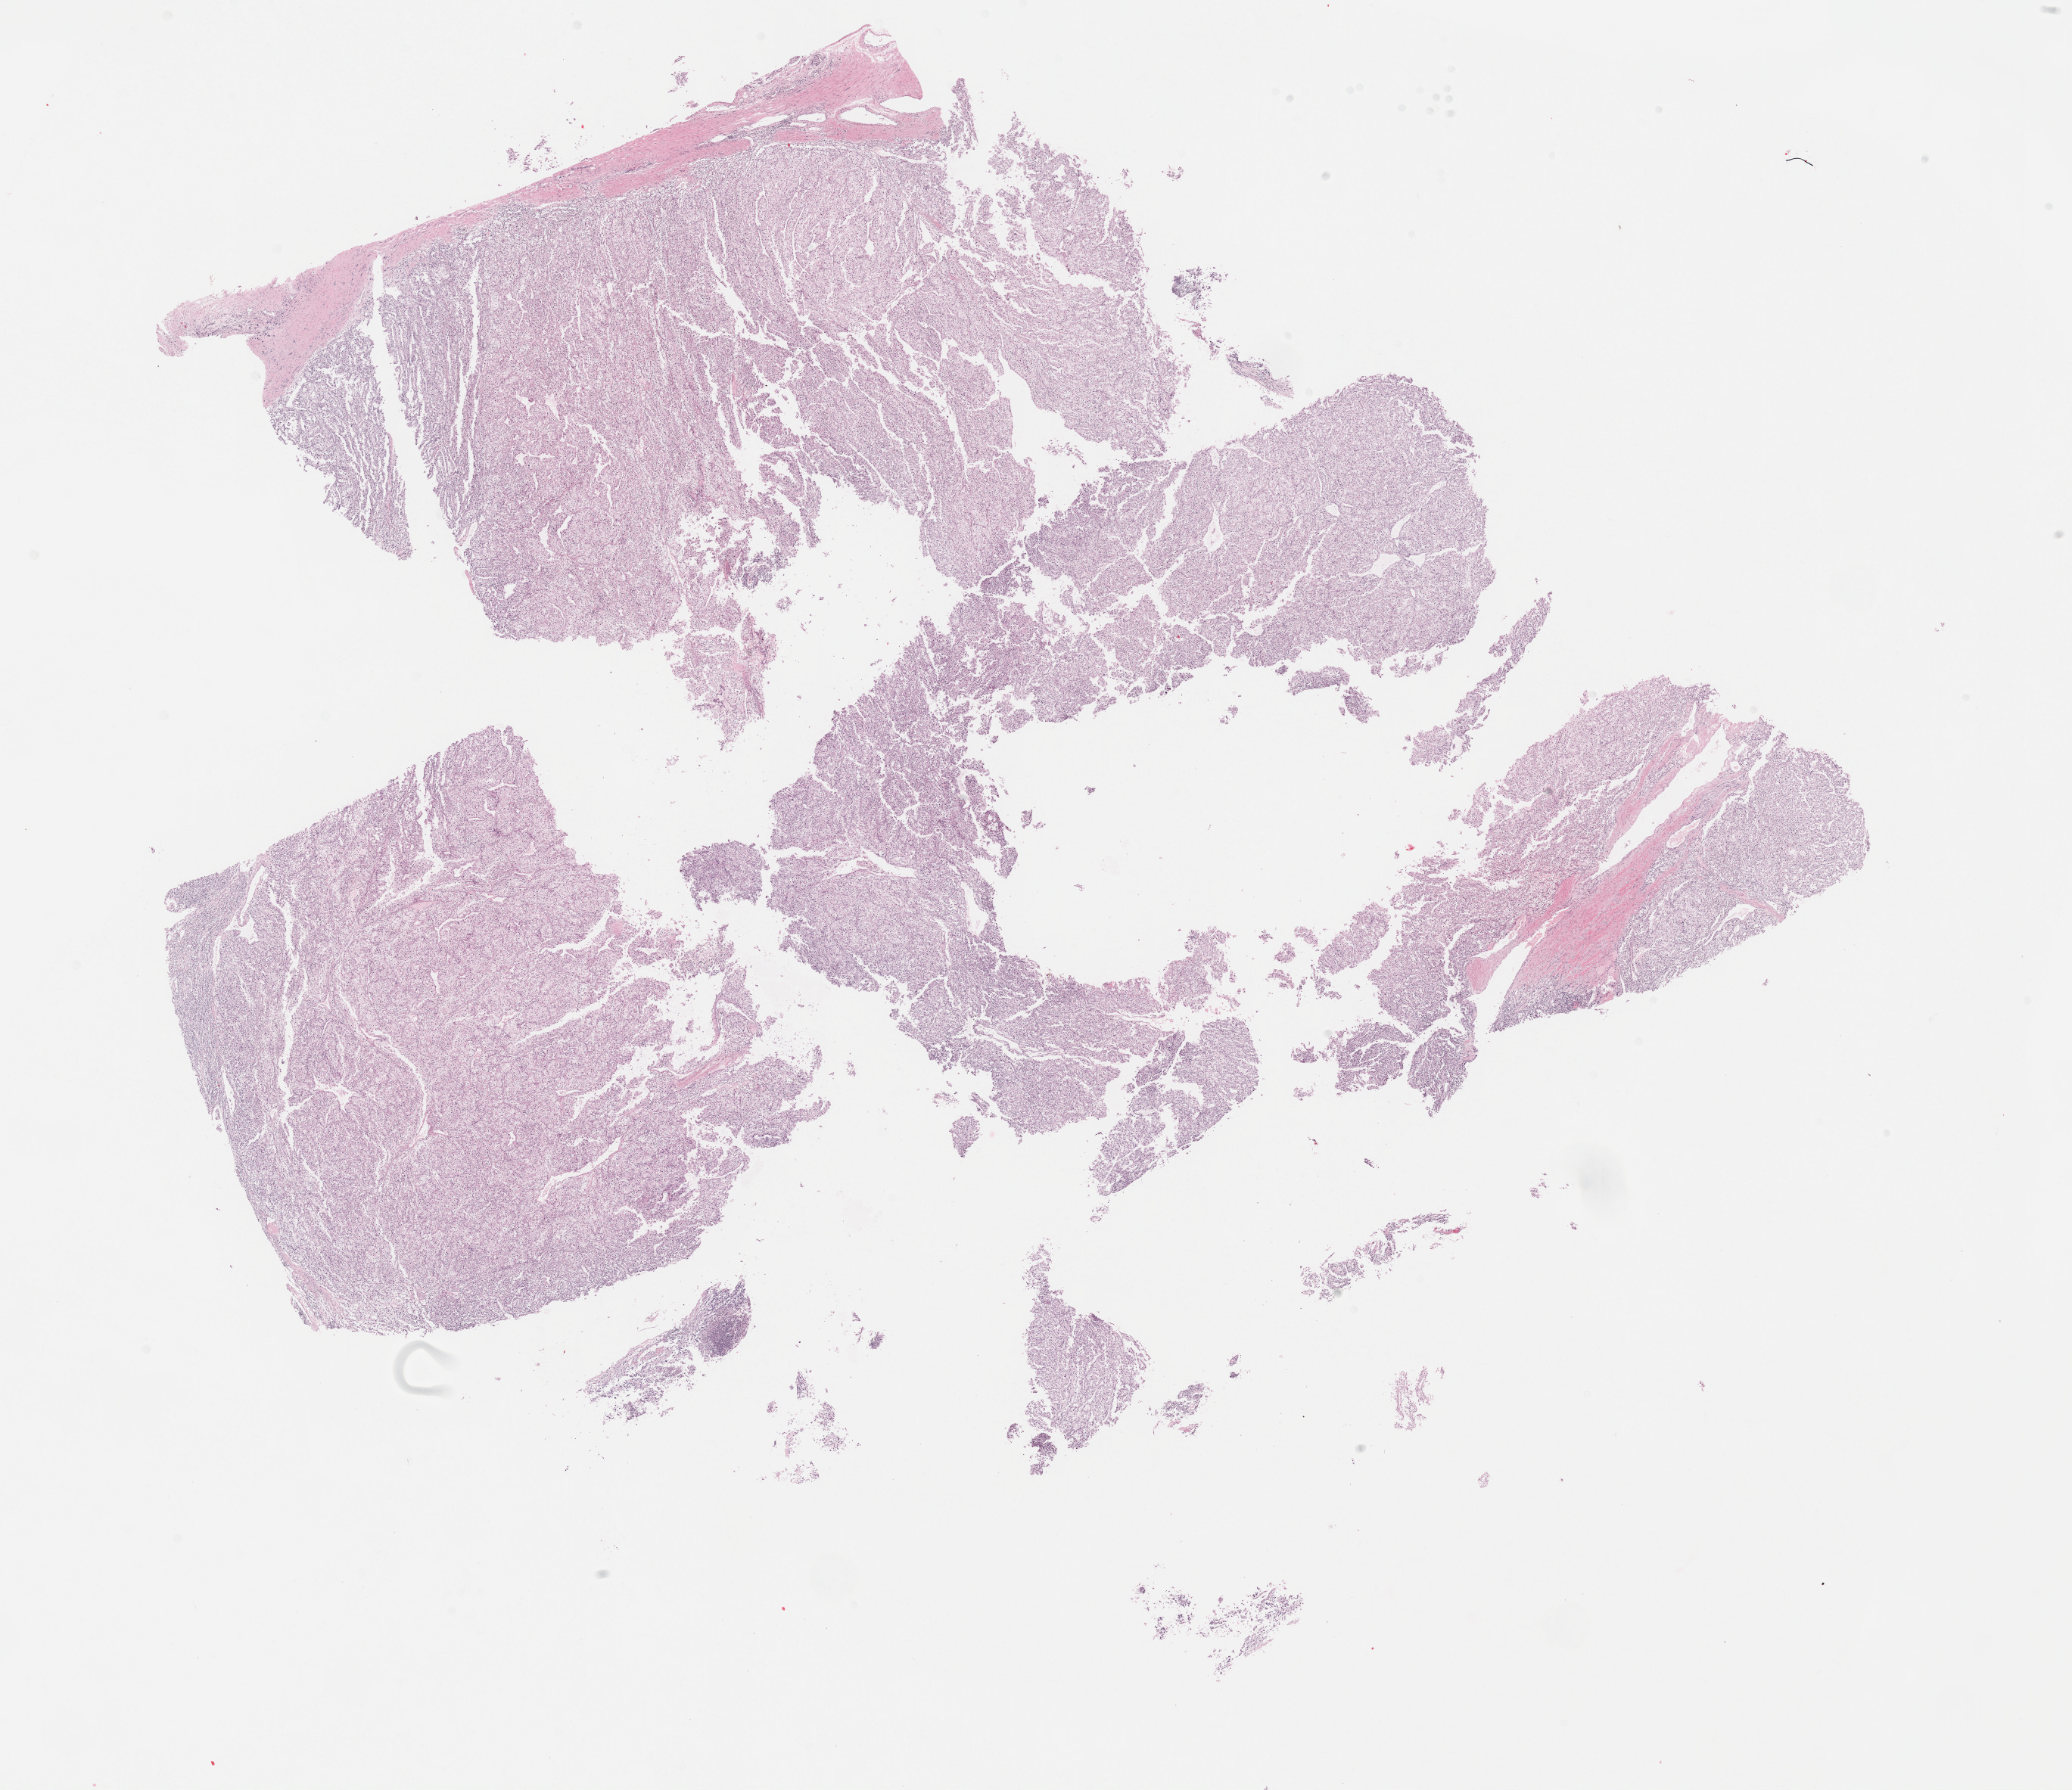
Whole-slide histology image, H&E-stained — low-resolution overview of the scanned area, about 22.1 x 19.1 mm (slide scanned at 40x); formalin-fixed paraffin-embedded (FFPE) diagnostic section; sample: primary tumour, kidney. Male, age 61 years at initial diagnosis. Histologic grade: G3 (poorly differentiated).
- laterality: left
- diagnosis: Clear cell adenocarcinoma, NOS
- AJCC pathologic stage: III
- lymph nodes positive (case pathology): 3 of 8 examined